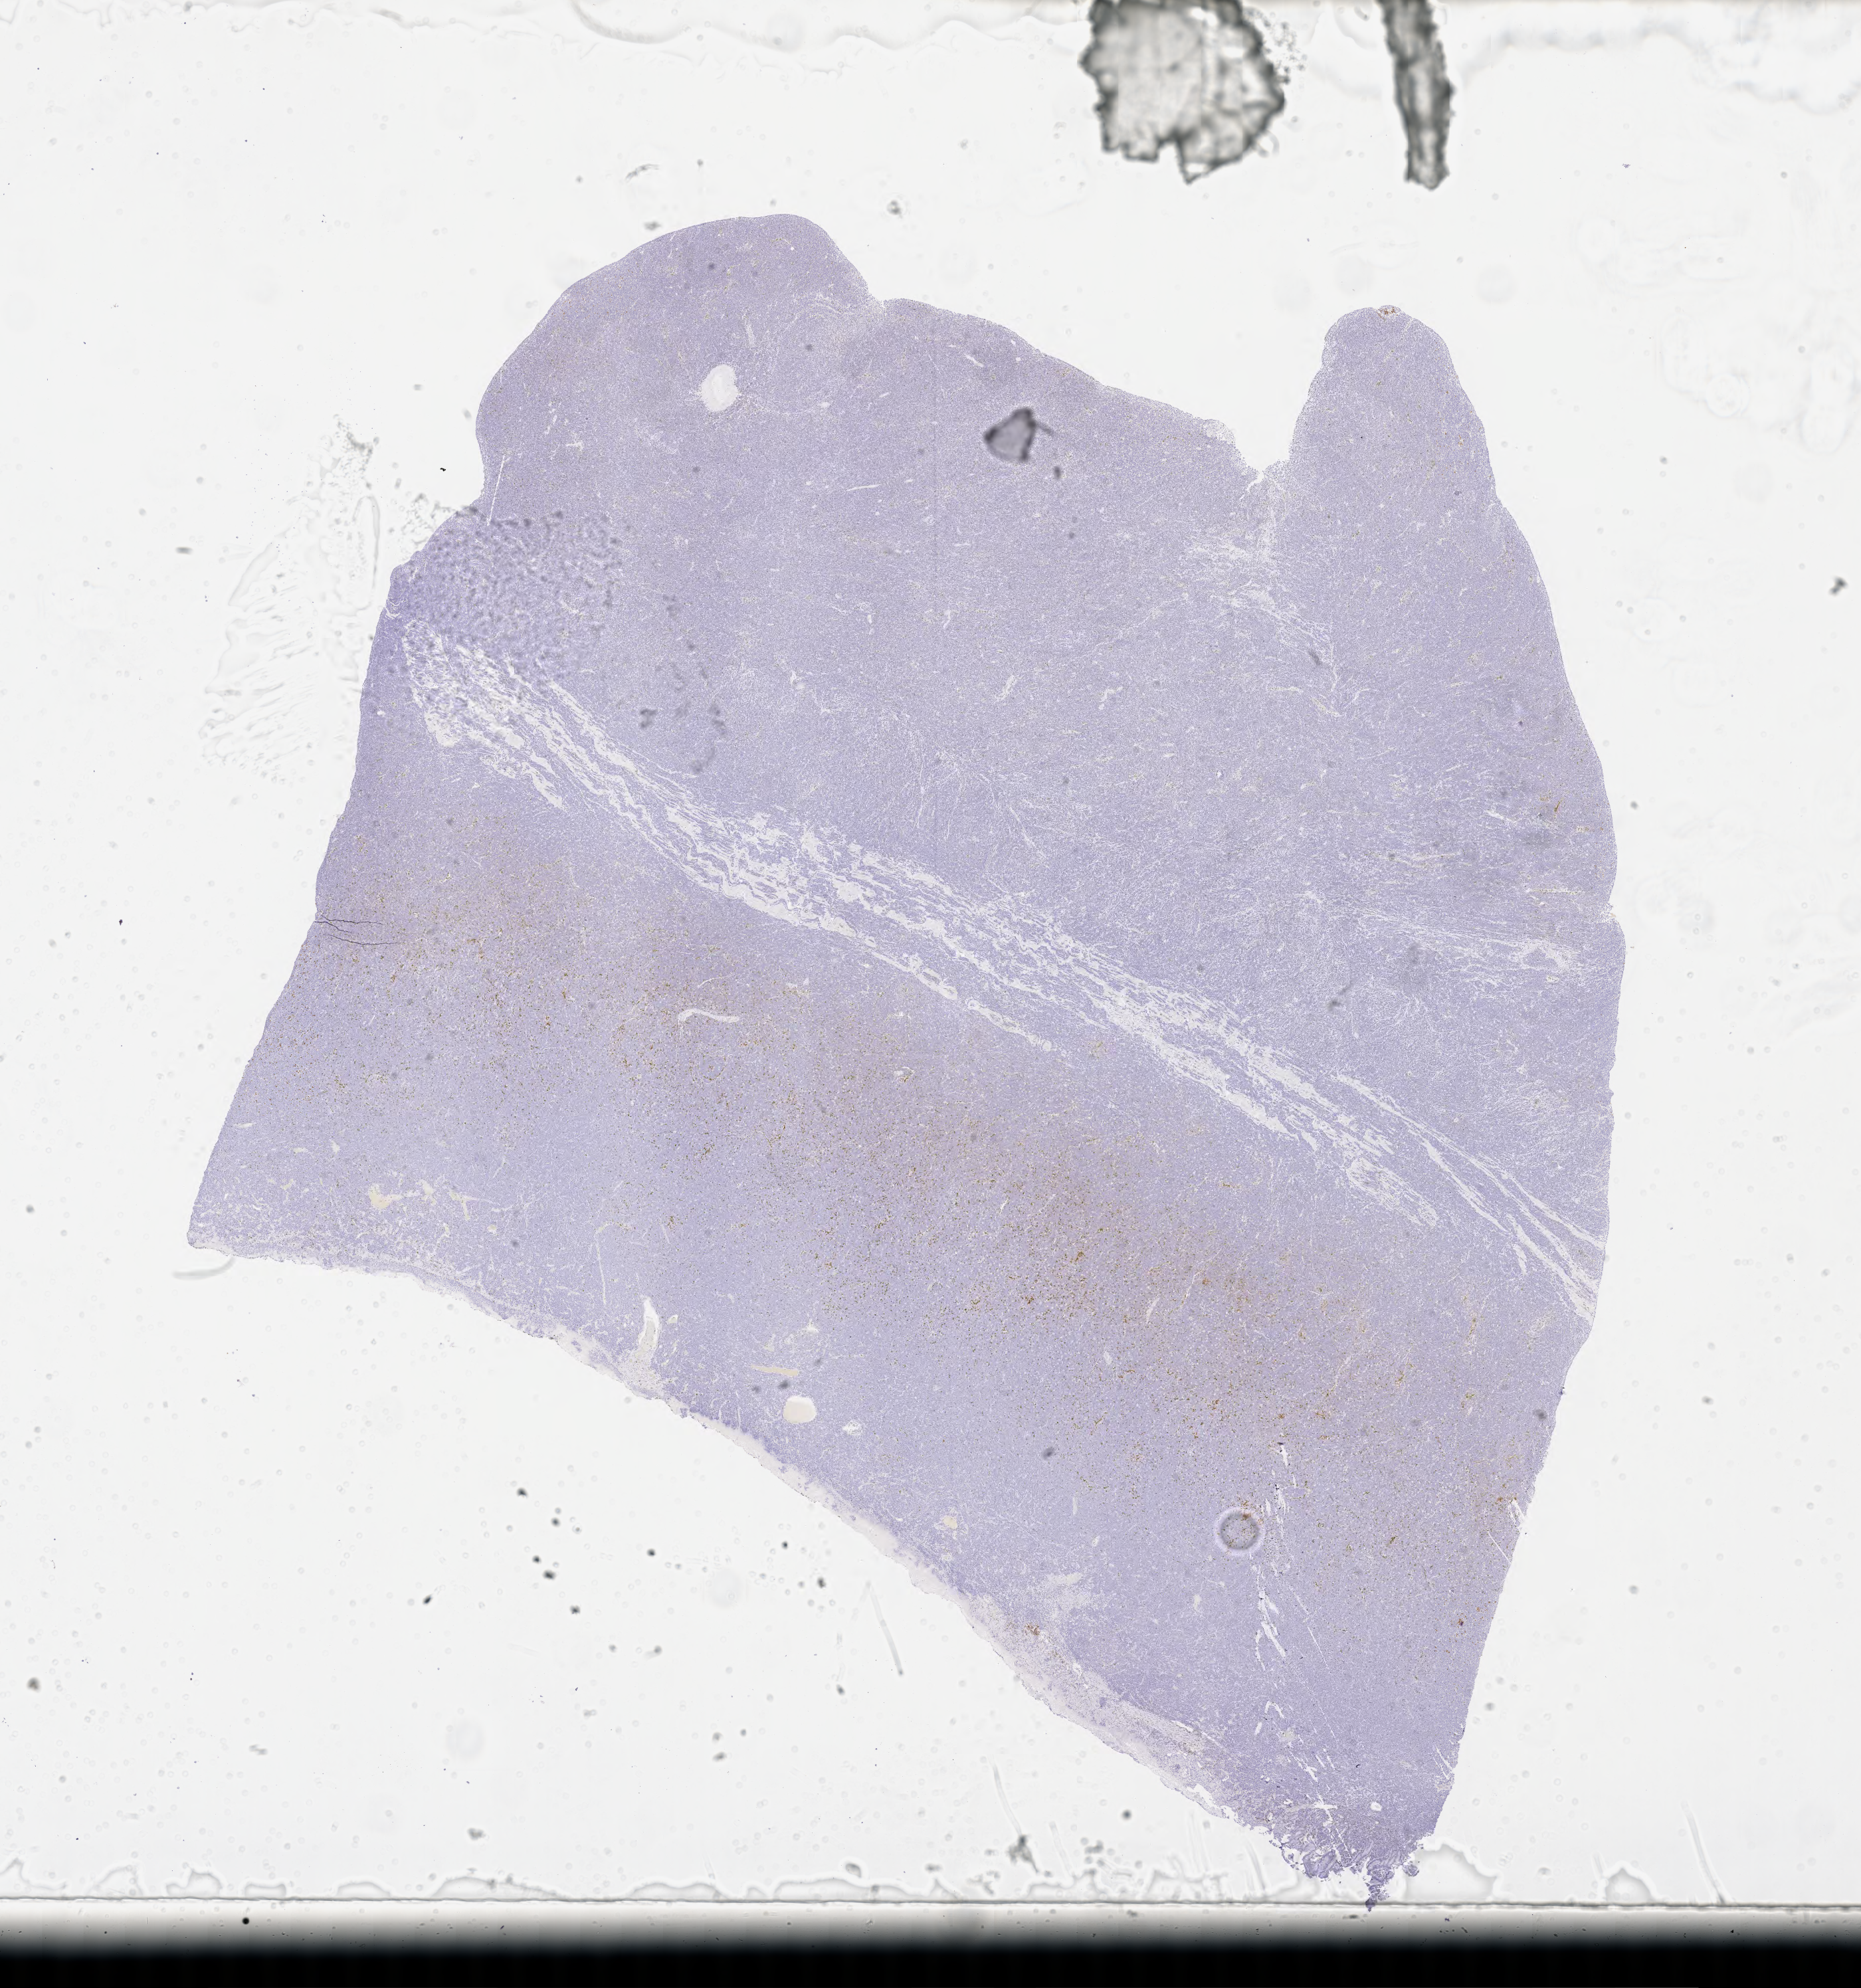
Immunohistochemistry (IHC) whole-slide image stained for CD5, a low-resolution overview of the entire scanned area, about 22.6 x 24.2 mm; specimen: tumor tissue. Male patient, age 36 years.
- histologic diagnosis: Burkitt lymphoma, NOS